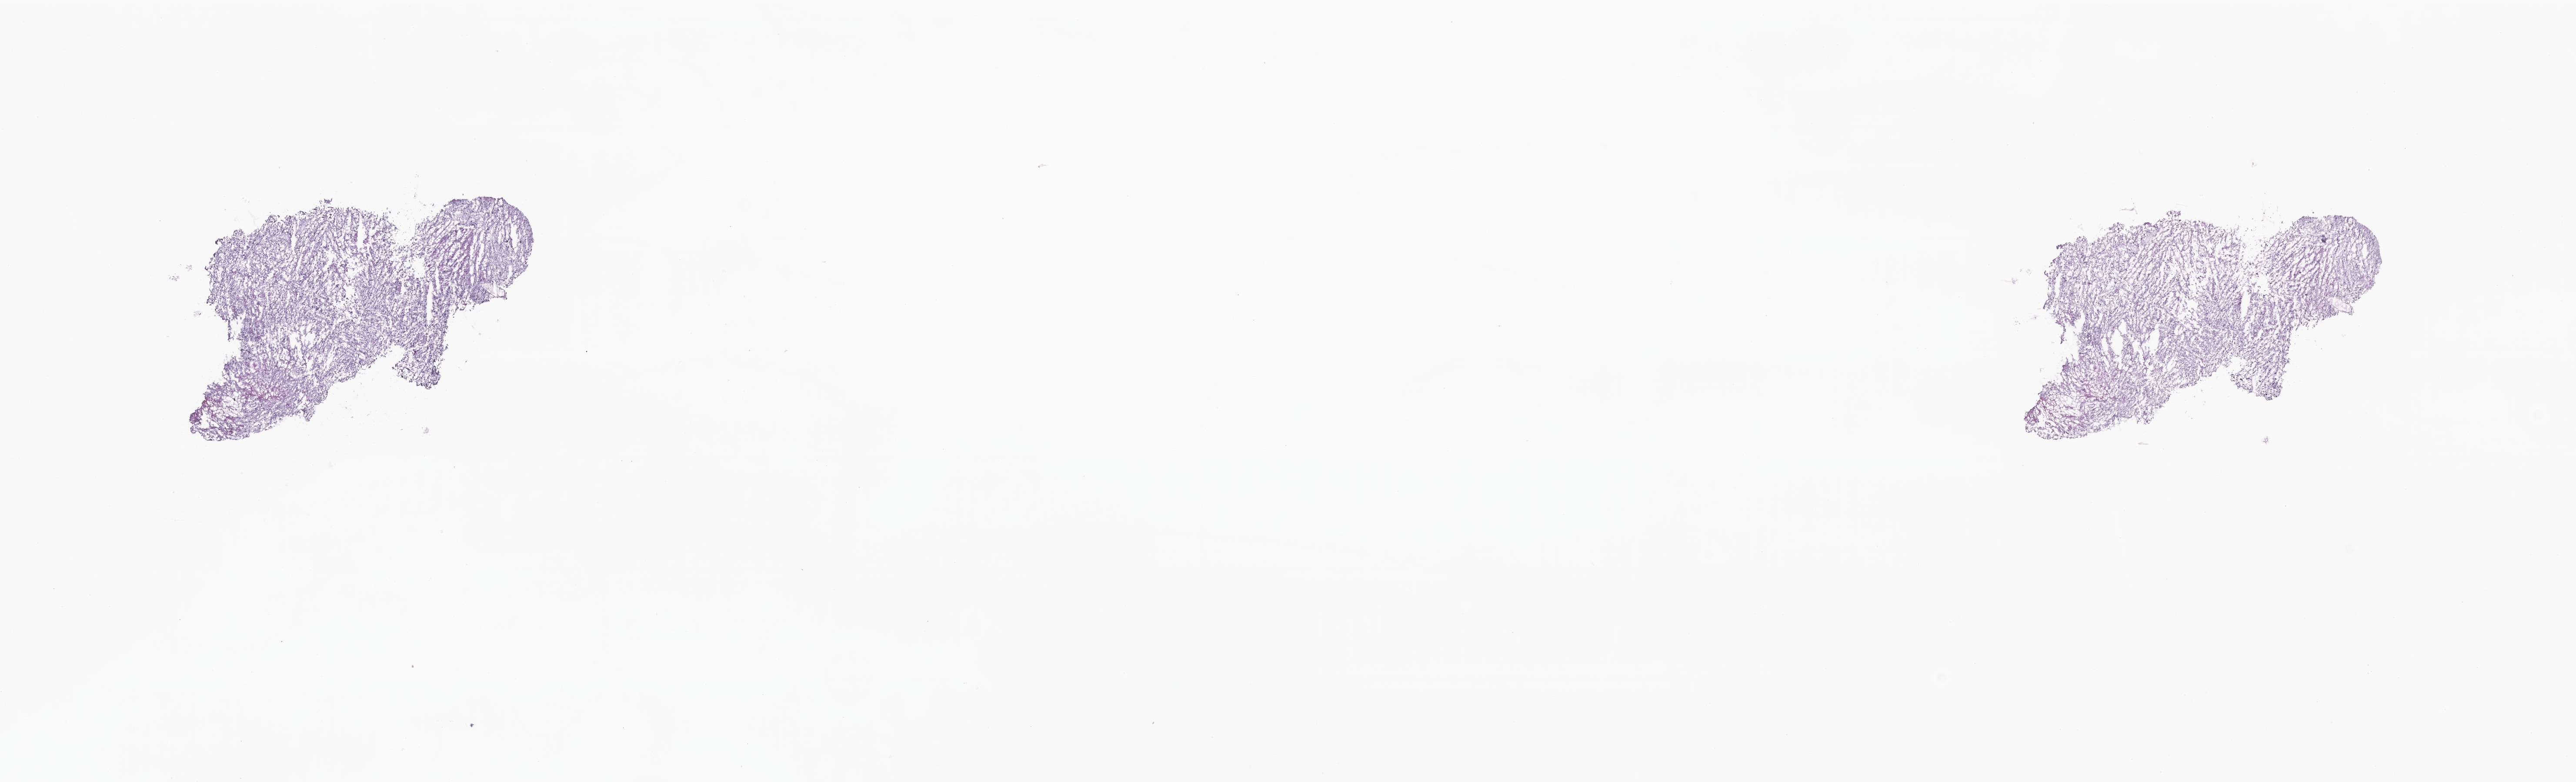
Whole-slide image, haematoxylin and eosin stain — a low-resolution overview of the entire scanned area, about 25.0 x 7.6 mm; frozen section; primary tumor; site: brain. Female patient; age at initial diagnosis 69 years. Composition of this section per pathologist review: tumor cells 79%, tumor nuclei 90%, stromal cells 8%, necrosis 5%, normal cells 8%. Inflammatory infiltration, as recorded: lymphocyte infiltration 0%, monocyte infiltration 0%, neutrophil infiltration 0%.
• section: top of the tissue portion
• diagnosis: Glioblastoma, NOS